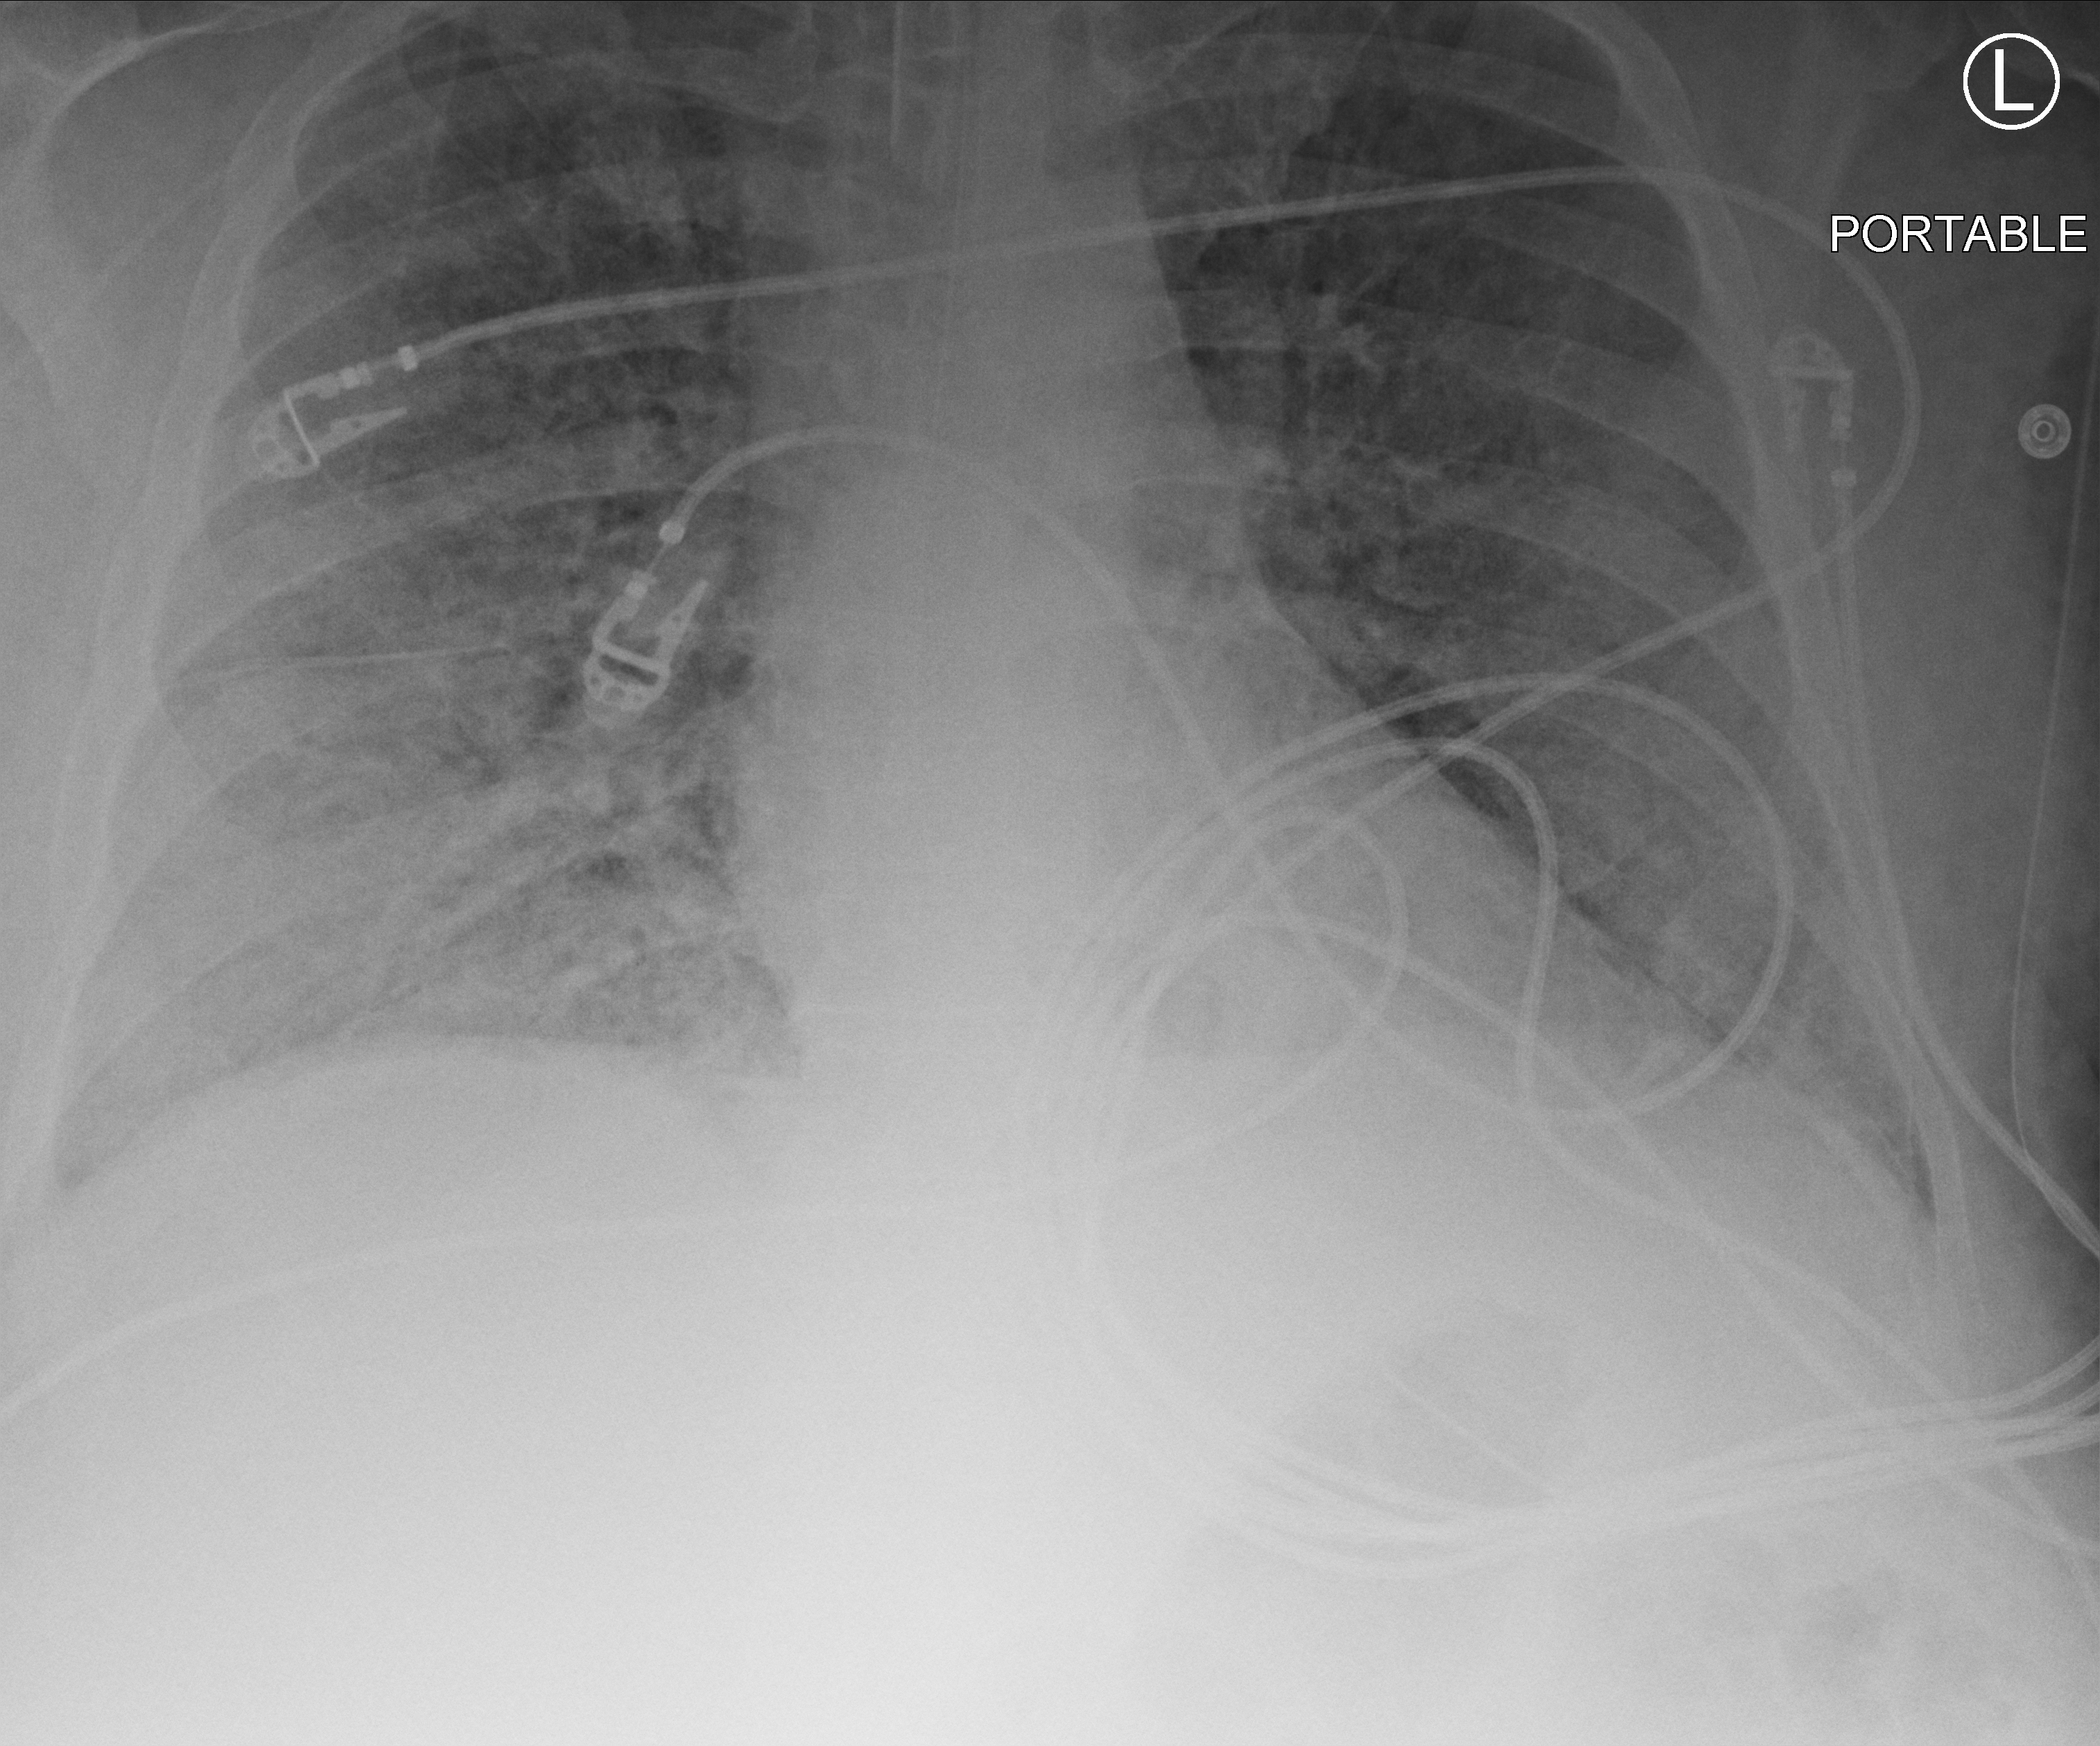
Bedside chest radiograph (computed radiography); anteroposterior (AP) projection. Patient hospitalised with COVID-19, aged 18–59 years.
Admission-level facts for this patient (not findings on this image; timing relative to this image not recorded): other chronic lung disease (admission record): no; smoking status (admission record): never; mechanically ventilated during this hospital stay: yes.